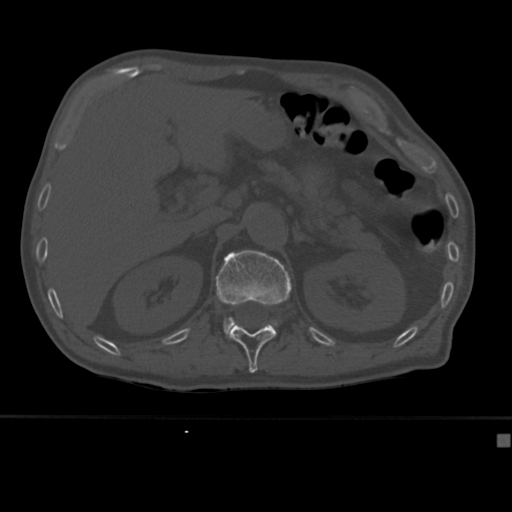
CT including the spine, one axial slice; position 181 of 430 along the scan axis; reconstruction kernel Br40s; bone window (W 1800 / L 400 HU); 512 × 512 image matrix, field of view 337 × 337 mm. Patient: male, 64 years. Case-level facts recorded for this patient, not image findings: primary cancer: uterus; vertebrae with lytic lesions (as recorded): T1, T4, T5, T7, L5.
Outlined on this slice (semi-automatically segmented with operator editing):
- L1 vertebra: bounding box [x1, y1, x2, y2] px = [215, 250, 292, 340]
- T12 vertebra: [230, 324, 277, 373]